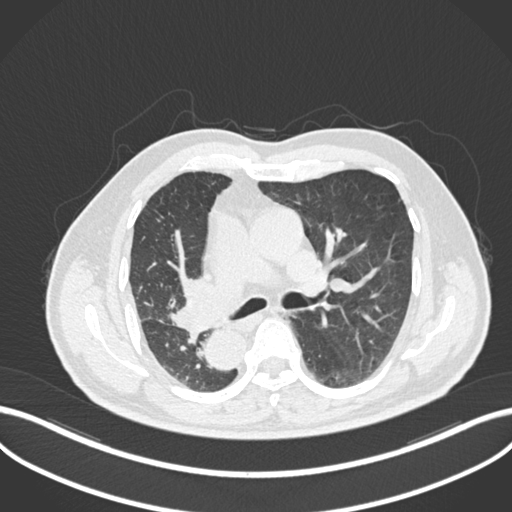
Chest CT, one axial slice; slice 136 of 206 in the series (ordered by position); lung window (W 1500 / L -600 HU); 1 mm slice thickness; 512 × 512 image matrix, field of view 400 × 400 mm. Patient: male, 67 years. From the clinical record (not read from this slice): clinical TNM (as recorded): T2a N0 M0.
Structures marked on this image (bounding box drawn by a radiologist):
- lung tumour (recorded histology: squamous cell carcinoma): bounding box [x1, y1, x2, y2] px = [166, 273, 223, 337]